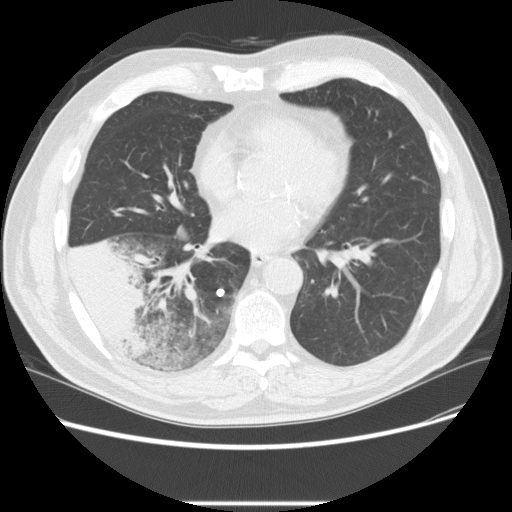
Low-dose screening chest CT, one axial slice. Reconstruction kernel STANDARD. 120 kVp. Lung window (W 1500 / L -600 HU). 2.5 mm slice thickness. 512 × 512 image matrix, field of view 380 × 380 mm.
Annotated regions visible in this slice (outlined manually by an expert reader):
- lesion 3 (tumor, lower lobe of right lung): bounding box (x1, y1, x2, y2) in pixels: (68, 239, 149, 360)